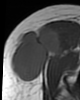
MRI of an extremity soft-tissue mass, one axial slice. Position 26 of 46 along the scan axis. MR volume resampled by the dataset authors to the PET/CT grid (not the native acquisition matrix). 3.27 mm slice thickness. 80 × 100 image matrix, field of view 78 × 98 mm. Female patient. From the clinical record (not read from this slice): histological type: synovial sarcoma; grade: intermediate; site of the primary tumour: right thigh.
Annotated regions visible in this slice (expert contour drawn on MRI and transferred to this co-registered scan by the dataset authors):
- gross tumour volume including surrounding oedema: bounding box (x1, y1, x2, y2) in pixels: (10, 26, 63, 84)
- gross tumour volume (mass): (10, 26, 63, 82)